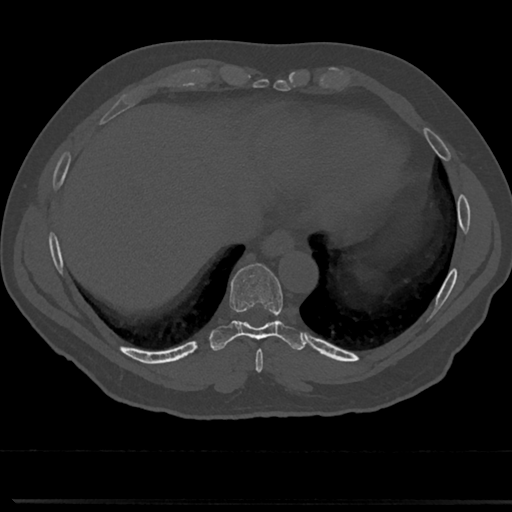
CT including the spine, one axial slice; position 307 of 817 along the scan axis; bone window (W 1800 / L 400 HU); 0.5 mm slice thickness; 512 × 512 image matrix, field of view 355 × 355 mm. Male patient, age 61 years. Case-level facts recorded for this patient, not image findings: primary cancer: prostate.
Annotated regions visible in this slice (semi-automatically segmented with operator editing):
- T8 vertebra: bounding box [x1, y1, x2, y2] px = [232, 295, 287, 354]
- T9 vertebra: [232, 267, 283, 329]